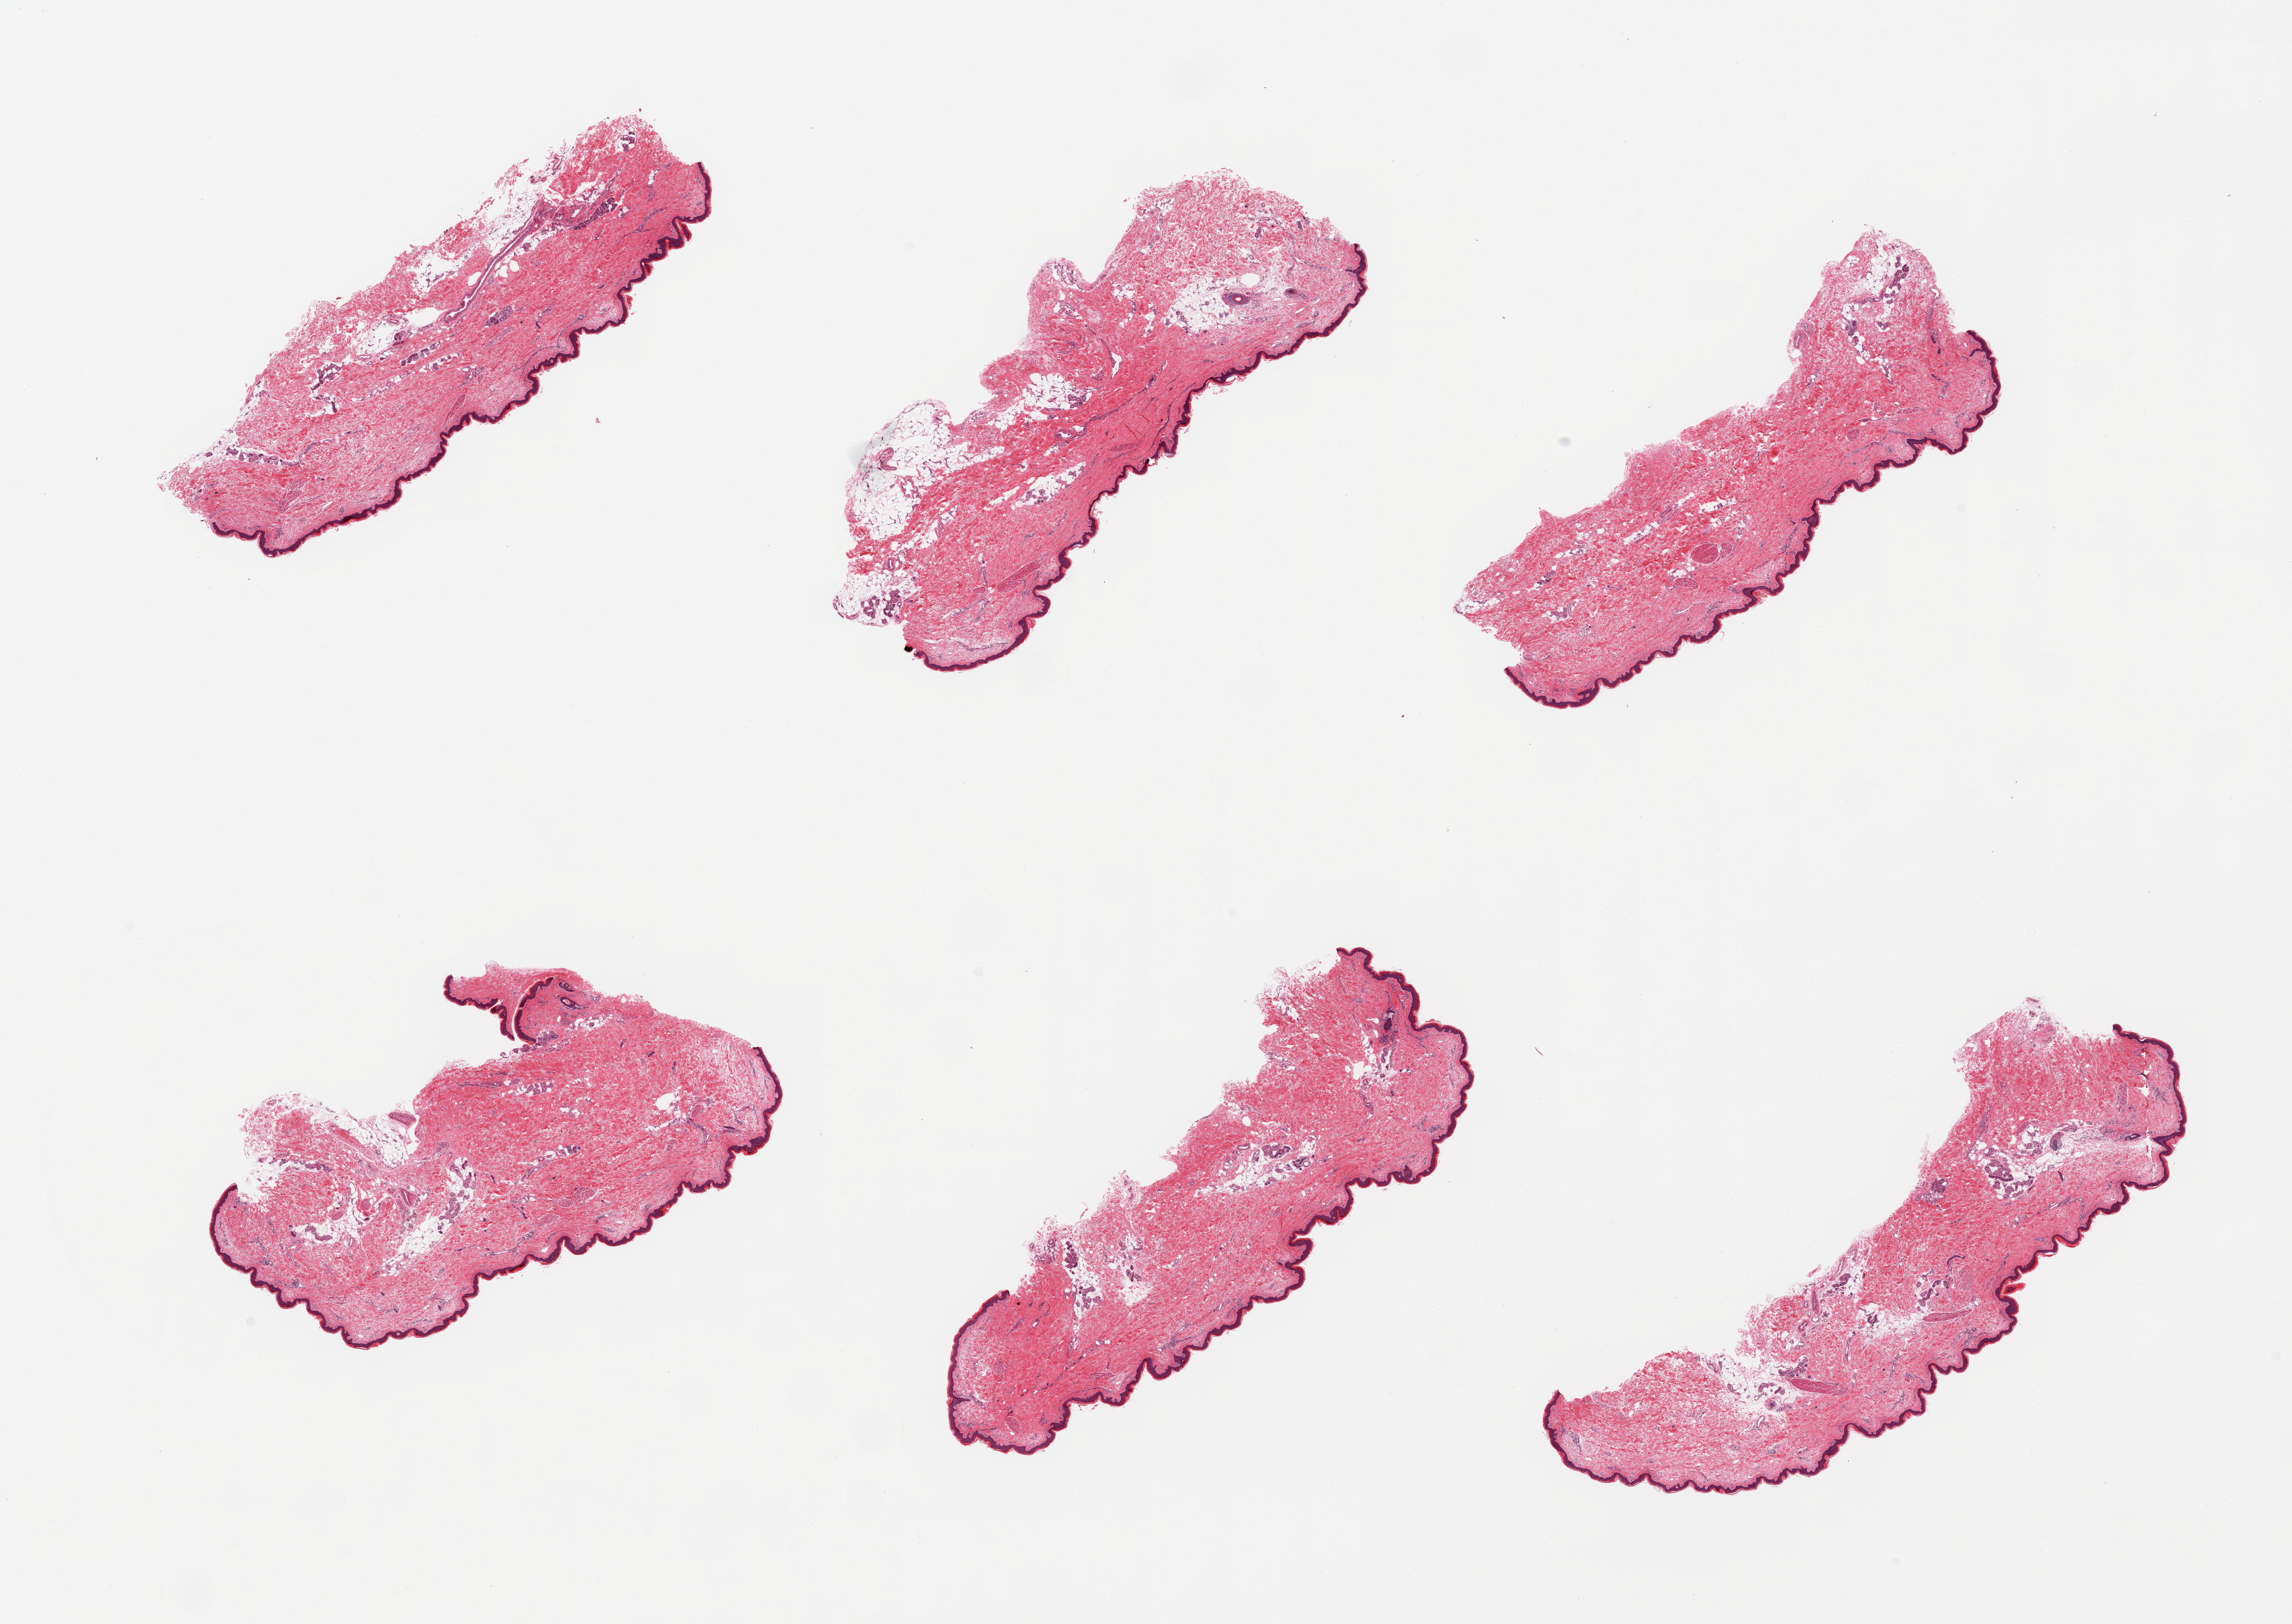
Digitized H&E-stained section, whole scanned area (about 27.6 x 19.5 mm) shown as a low-resolution overview, PAXgene-fixed, paraffin-embedded tissue, section of skin of lower leg (target tissue), tissue donor sample. Female donor.
Reviewer comment on this tissue sample: 6 pieces; 10% intradermal fat.